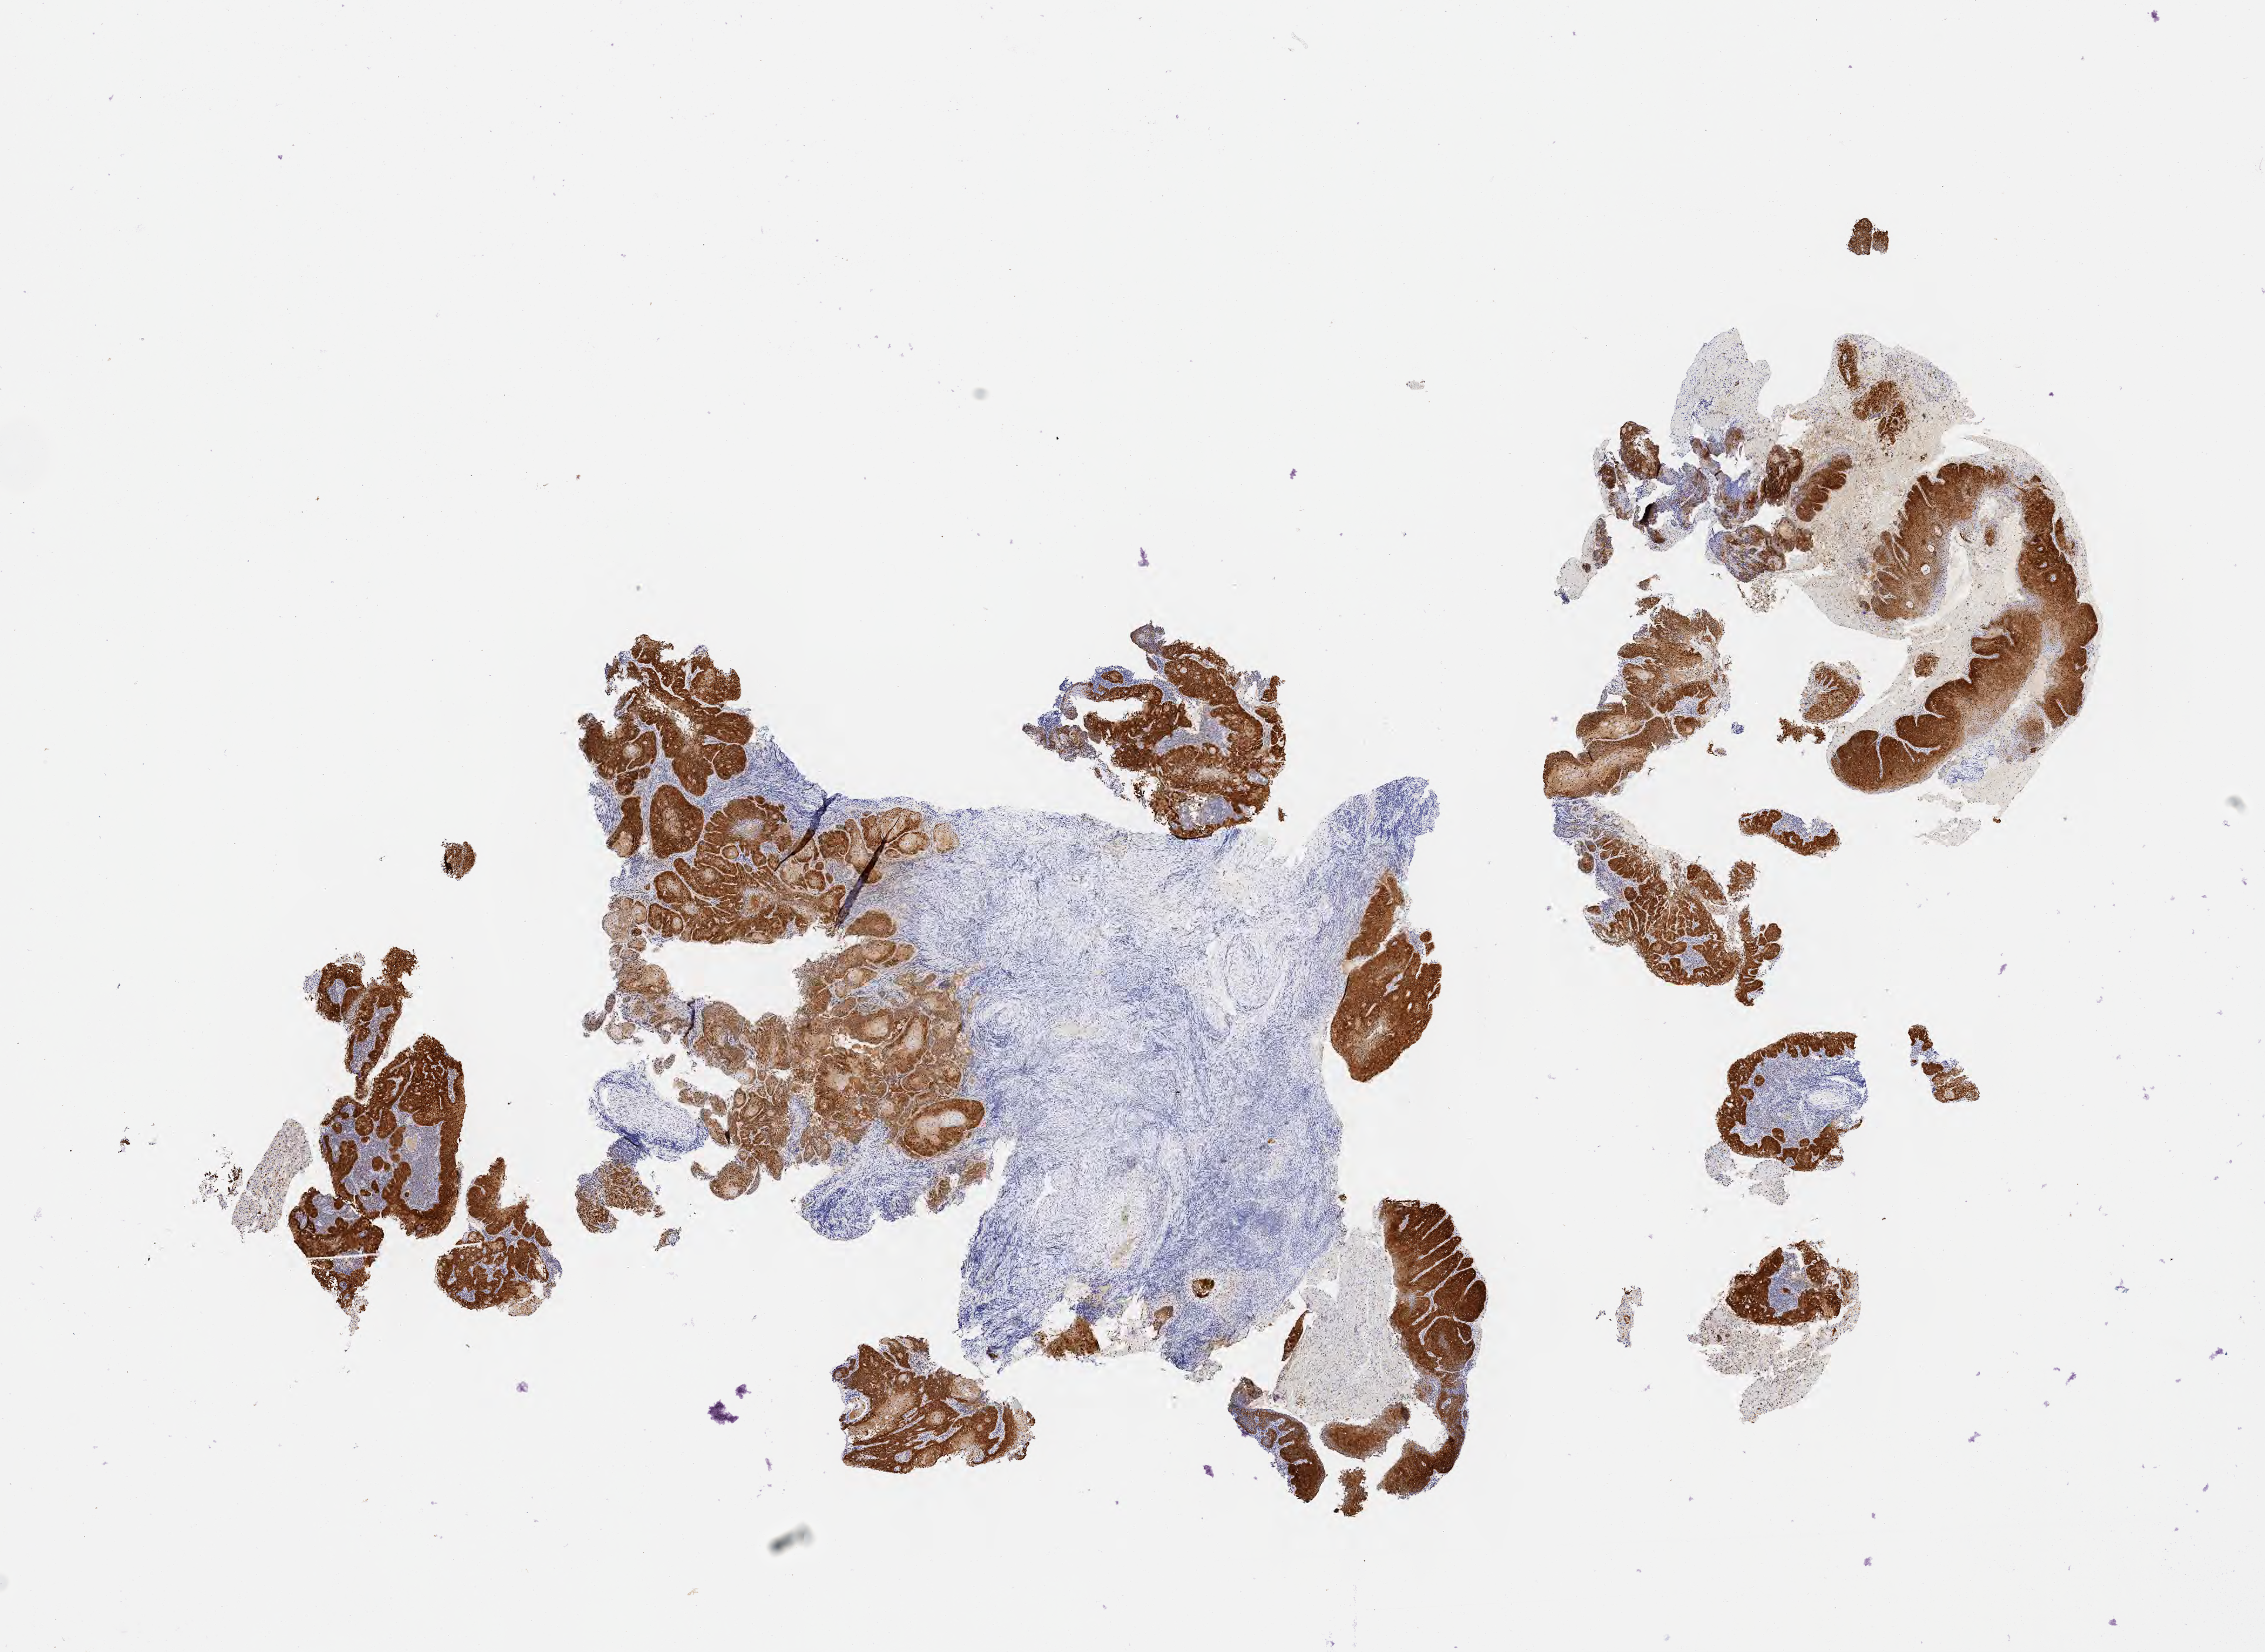
Immunohistochemistry (IHC) whole-slide image stained for p16 (p16INK4a) — whole scanned area (about 15.6 x 11.4 mm) shown as a low-resolution overview, specimen: tumor tissue, site: cervix. Patient: female, 60 years old.
Diagnosis: Squamous cell carcinoma, keratinizing, NOS.